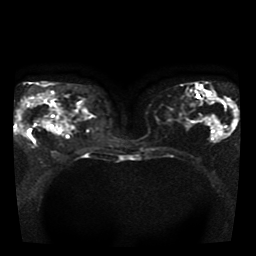
Breast MRI, one axial slice; position 20 of 41 along the scan axis; diffusion-weighted series; image 2 of 4 stored at this slice position (different b-values; order by instance number); 1.5 T; 5 mm slice thickness; 256 × 256 image matrix. Female patient.
Outlined on this slice (manually delineated by an expert):
- tumour on diffusion-weighted imaging: bounding box [x1, y1, x2, y2] px = [19, 99, 36, 133]